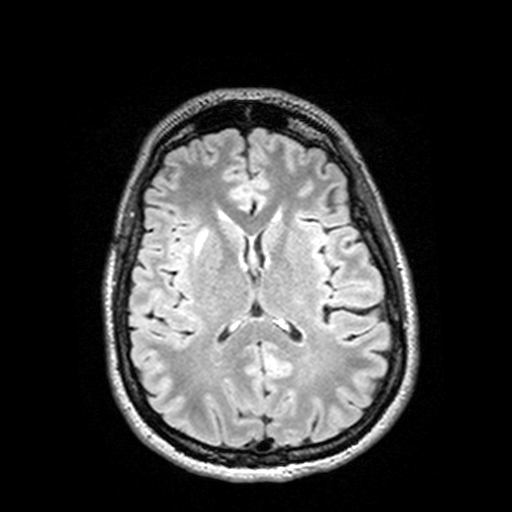
Brain MRI from a brain-tumour surgery series, one axial slice; slice 62 of 144 in the series (ordered by position); T2 FLAIR; 512 × 512 image matrix, field of view 250 × 250 mm. From the clinical record (not read from this slice): histopathology: Astrocytoma; WHO grade: 3; IDH mutation: yes; tumour location: Right Insular Temporal.
Structures marked on this image (expert manual segmentation):
- tumour: box from (x=190, y=228) to (x=210, y=248) px